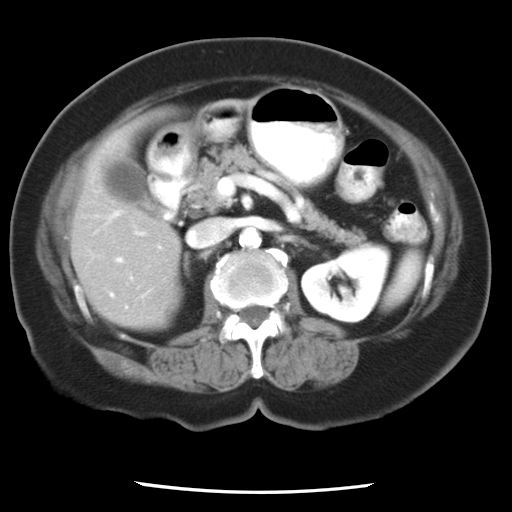
Contrast-enhanced abdominal CT, one axial slice. Slice 10 of 24 in the series (ordered by position). 120 kVp. Intravenous contrast given. Soft-tissue window (W 400 / L 40 HU). 7.5 mm slice thickness. 512 × 512 image matrix, field of view 312 × 312 mm. Female patient, age 71 years. Case-level facts recorded for this patient, not image findings: diagnosis: colorectal cancer liver metastases, imaged before liver resection; multiple liver metastases: no; largest metastasis: 4.3 cm; disease in both lobes: no.
Structures marked on this image (expert manual segmentation):
- hepatic veins: bounding box [x1, y1, x2, y2] px = [110, 294, 113, 296]
- liver: [70, 111, 180, 329]
- planned liver remnant (the part of the liver to remain after resection): [70, 114, 180, 329]
- portal vein (with intrahepatic branches): [115, 245, 162, 264]